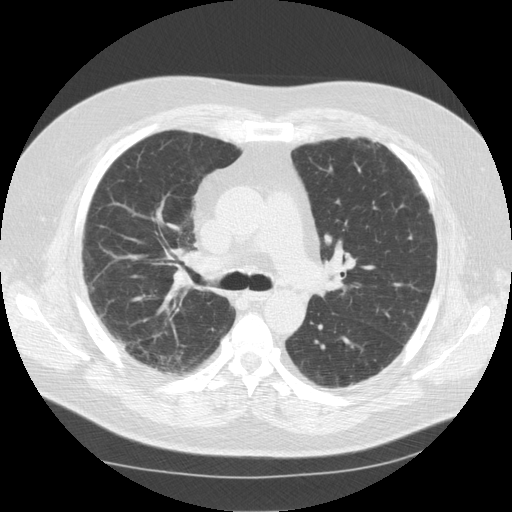
Low-dose screening chest CT, axial slice. Third annual screen. Lung window (W 1500 / L -600 HU). Standard (soft-tissue) reconstruction kernel (STANDARD). 512 × 512 image matrix, field of view 380 × 380 mm. Male, age 56 years at enrolment. Current smoker at enrolment.
Lesion marked by an expert reader, box from (x=107, y=325) to (x=135, y=365) px. The screening reader recorded 2 non-calcified nodules or masses ≥4 mm on this exam (right upper lobe, right lower lobe); which of them this box marks is not recorded. Lung cancer was diagnosed 66 days after this screen: large cell neuroendocrine carcinoma, right upper lobe, stage IIIA (AJCC 6th edition), 10 mm at pathology.